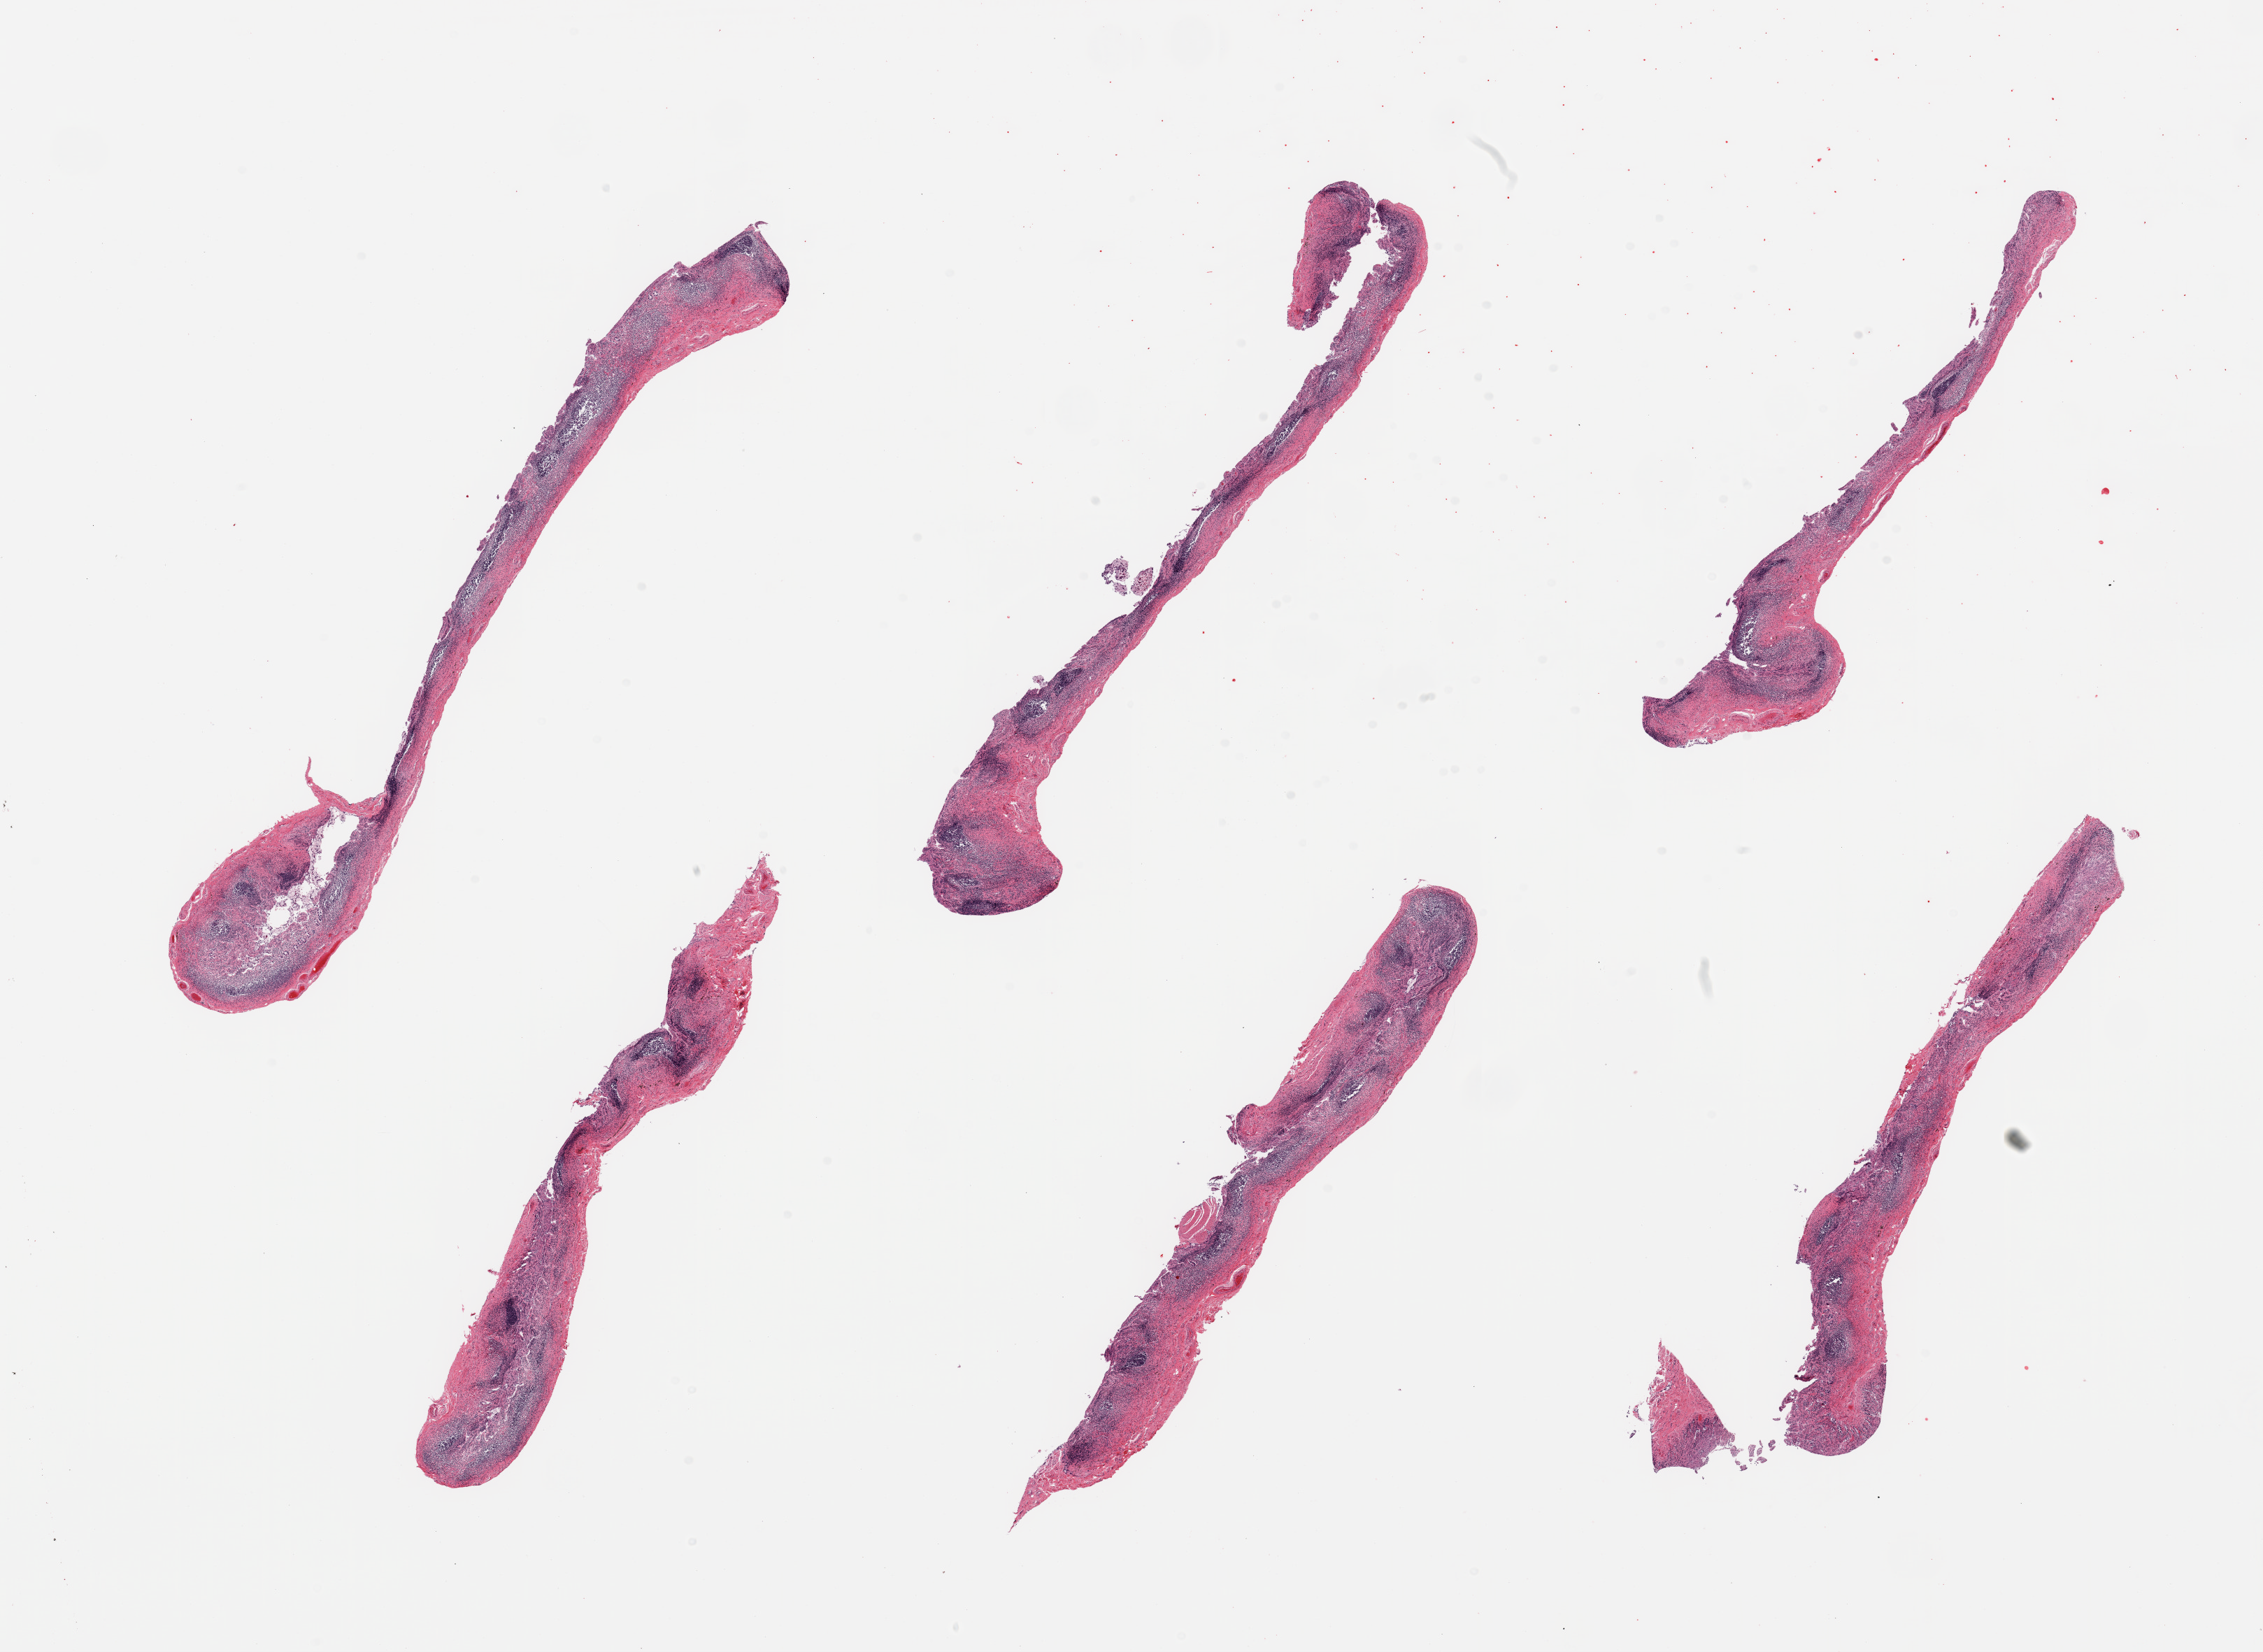
Hematoxylin and eosin (H&E) whole-slide image, shown as a low-resolution overview of the whole scanned area (about 25.6 x 18.7 mm, slide scanned at 20x); PAXgene-fixed, paraffin-embedded tissue; section of ileum (target tissue); donor tissue sample.
• reviewer comment on this tissue sample: 6 pieces; lymphoid tissue is more diffuse than nodular; well dissected